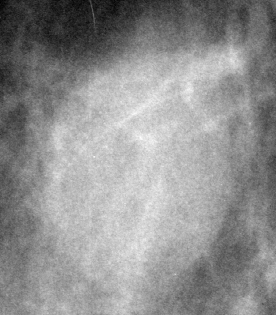
Cropped region of a digitized screen-film mammogram centred on a radiologist-marked abnormality, right breast, MLO view.
Finding: mass, shape oval, margins circumscribed; BI-RADS assessment category 3; pathology (as recorded): benign.